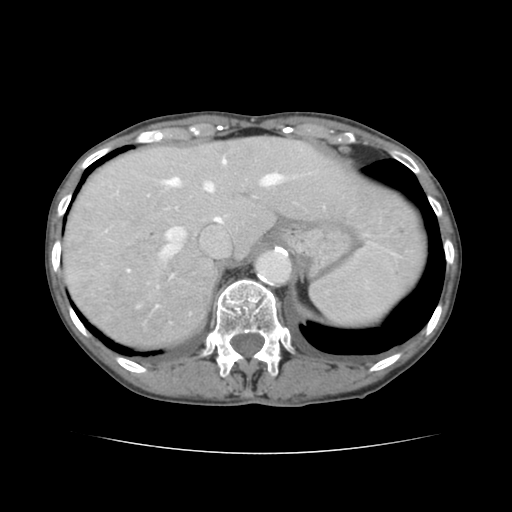
Contrast-enhanced abdominal CT, one axial slice; position 111 of 136 along the scan axis; 120 kVp; intravenous contrast given; soft-tissue window (W 400 / L 40 HU); 2.5 mm slice thickness; 512 × 512 image matrix, field of view 319 × 319 mm. Female patient, age 77 years. Case-level facts recorded for this patient, not image findings: diagnosis: colorectal cancer liver metastases, imaged before liver resection.
Outlined on this slice (manually delineated by an expert):
- hepatic veins: bounding box (x1, y1, x2, y2) in pixels: (102, 160, 281, 265)
- liver: (63, 137, 423, 348)
- planned liver remnant (the part of the liver to remain after resection): (167, 137, 422, 277)
- portal vein (with intrahepatic branches): (322, 205, 326, 210)